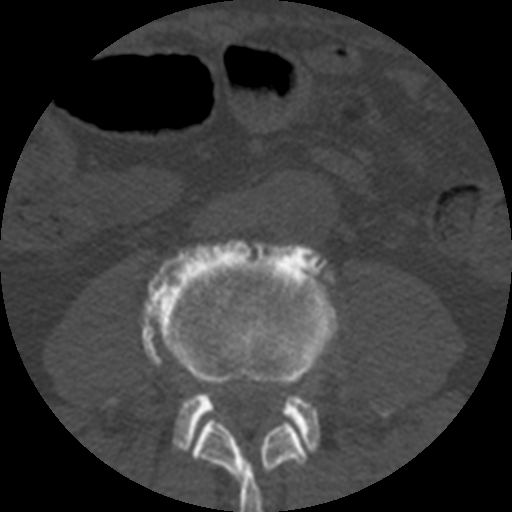
CT including the spine, one axial slice. Position 104 of 508 along the scan axis. Reconstruction kernel STANDARD. 120 kVp. Bone window (W 1800 / L 400 HU). 1.25 mm slice thickness. 512 × 512 image matrix, field of view 160 × 160 mm. Patient age 57 years. Case-level facts recorded for this patient, not image findings: primary cancer: prostate.
Structures marked on this image (semi-automatic segmentation, software-assisted and operator-edited):
- L3 vertebra: bounding box (x1, y1, x2, y2) in pixels: (192, 419, 306, 512)
- L4 vertebra: (107, 240, 391, 454)